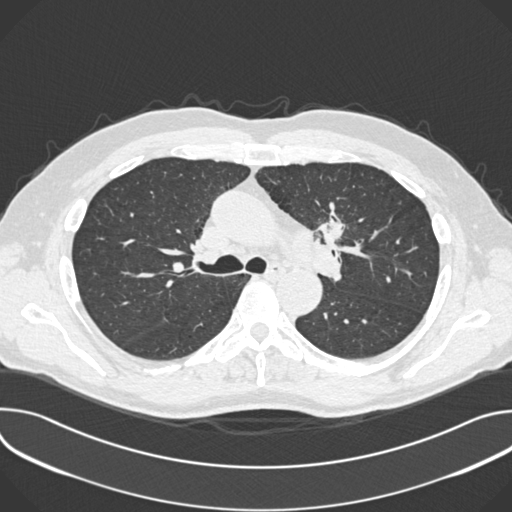
Low-dose screening chest CT, one axial slice. Slice 248 of 361 in the series (ordered by position). Reconstruction kernel B30f. 120 kVp. Lung window (W 1500 / L -600 HU). 1 mm slice thickness. 512 × 512 image matrix, field of view 380 × 380 mm.
Annotated regions visible in this slice (expert manual segmentation):
- lesion 1 (tumor, upper lobe of left lung): bounding box (x1, y1, x2, y2) in pixels: (317, 212, 344, 248)